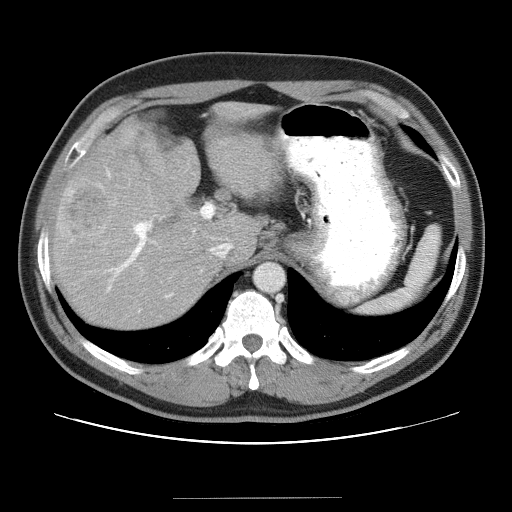
Contrast-enhanced abdominal CT (liver protocol), one axial slice; slice 26 of 40 in the series (ordered by position); 120 kVp; soft-tissue window (W 400 / L 40 HU); 5 mm slice thickness; 512 × 512 image matrix, field of view 380 × 380 mm. From the clinical record (not read from this slice): diagnosis: hepatocellular carcinoma (patient treated with transarterial chemoembolisation; whether this scan precedes or follows treatment is not stated here); TNM stage (as recorded): Stage-IVA; Child-Pugh class: B.
Structures marked on this image (semi-automatic segmentation, software-assisted and operator-edited):
- abdominal aorta: bounding box (x1, y1, x2, y2) in pixels: (255, 263, 282, 291)
- liver parenchyma outside the tumour (the mass and vessels are separate outlines, so this box may not span the whole liver): (50, 106, 274, 328)
- mass: (57, 176, 118, 237)
- liver vessels: (107, 171, 173, 297)